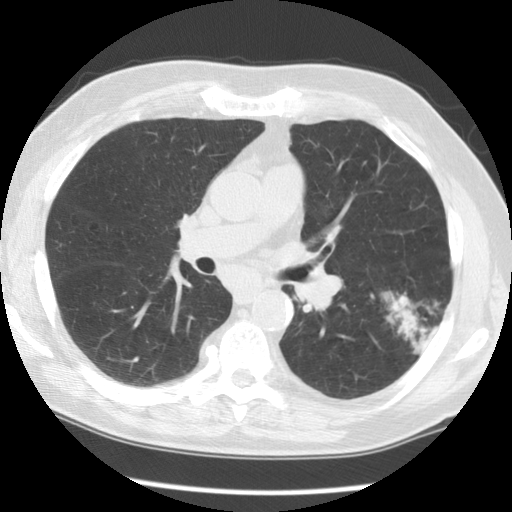
Low-dose screening chest CT, axial slice. Baseline annual screen. Lung window (W 1500 / L -600 HU). 2.5 mm slice thickness. Standard (soft-tissue) reconstruction kernel (STANDARD). Slice 54 of 130 in the series. Male, age 71 years at enrolment. Former smoker at enrolment.
Expert reader's lesion annotation, bounding box [x1, y1, x2, y2] px = [372, 283, 458, 366]. The screening reader recorded 3 non-calcified nodules or masses ≥4 mm on this exam; which of them this box marks is not recorded. Later outcome: lung cancer diagnosed 42 days after this screen — small cell carcinoma, NOS, left lower lobe, poorly differentiated (G3), stage IIIA (AJCC 6th edition), 19 mm at pathology.